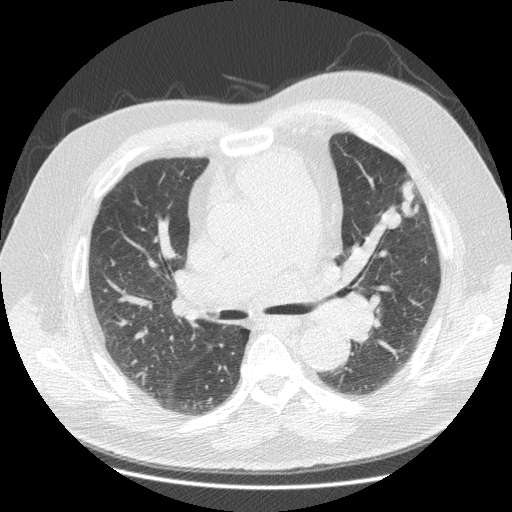
Low-dose screening chest CT, one axial slice. Position 64 of 116 along the scan axis. Reconstruction kernel STANDARD. 140 kVp. Lung window (W 1500 / L -600 HU). 2.5 mm slice thickness. 512 × 512 image matrix, field of view 390 × 390 mm.
Structures marked on this image (expert manual segmentation):
- lesion 1 (tumor, upper lobe of left lung): bounding box [x1, y1, x2, y2] px = [381, 180, 419, 229]